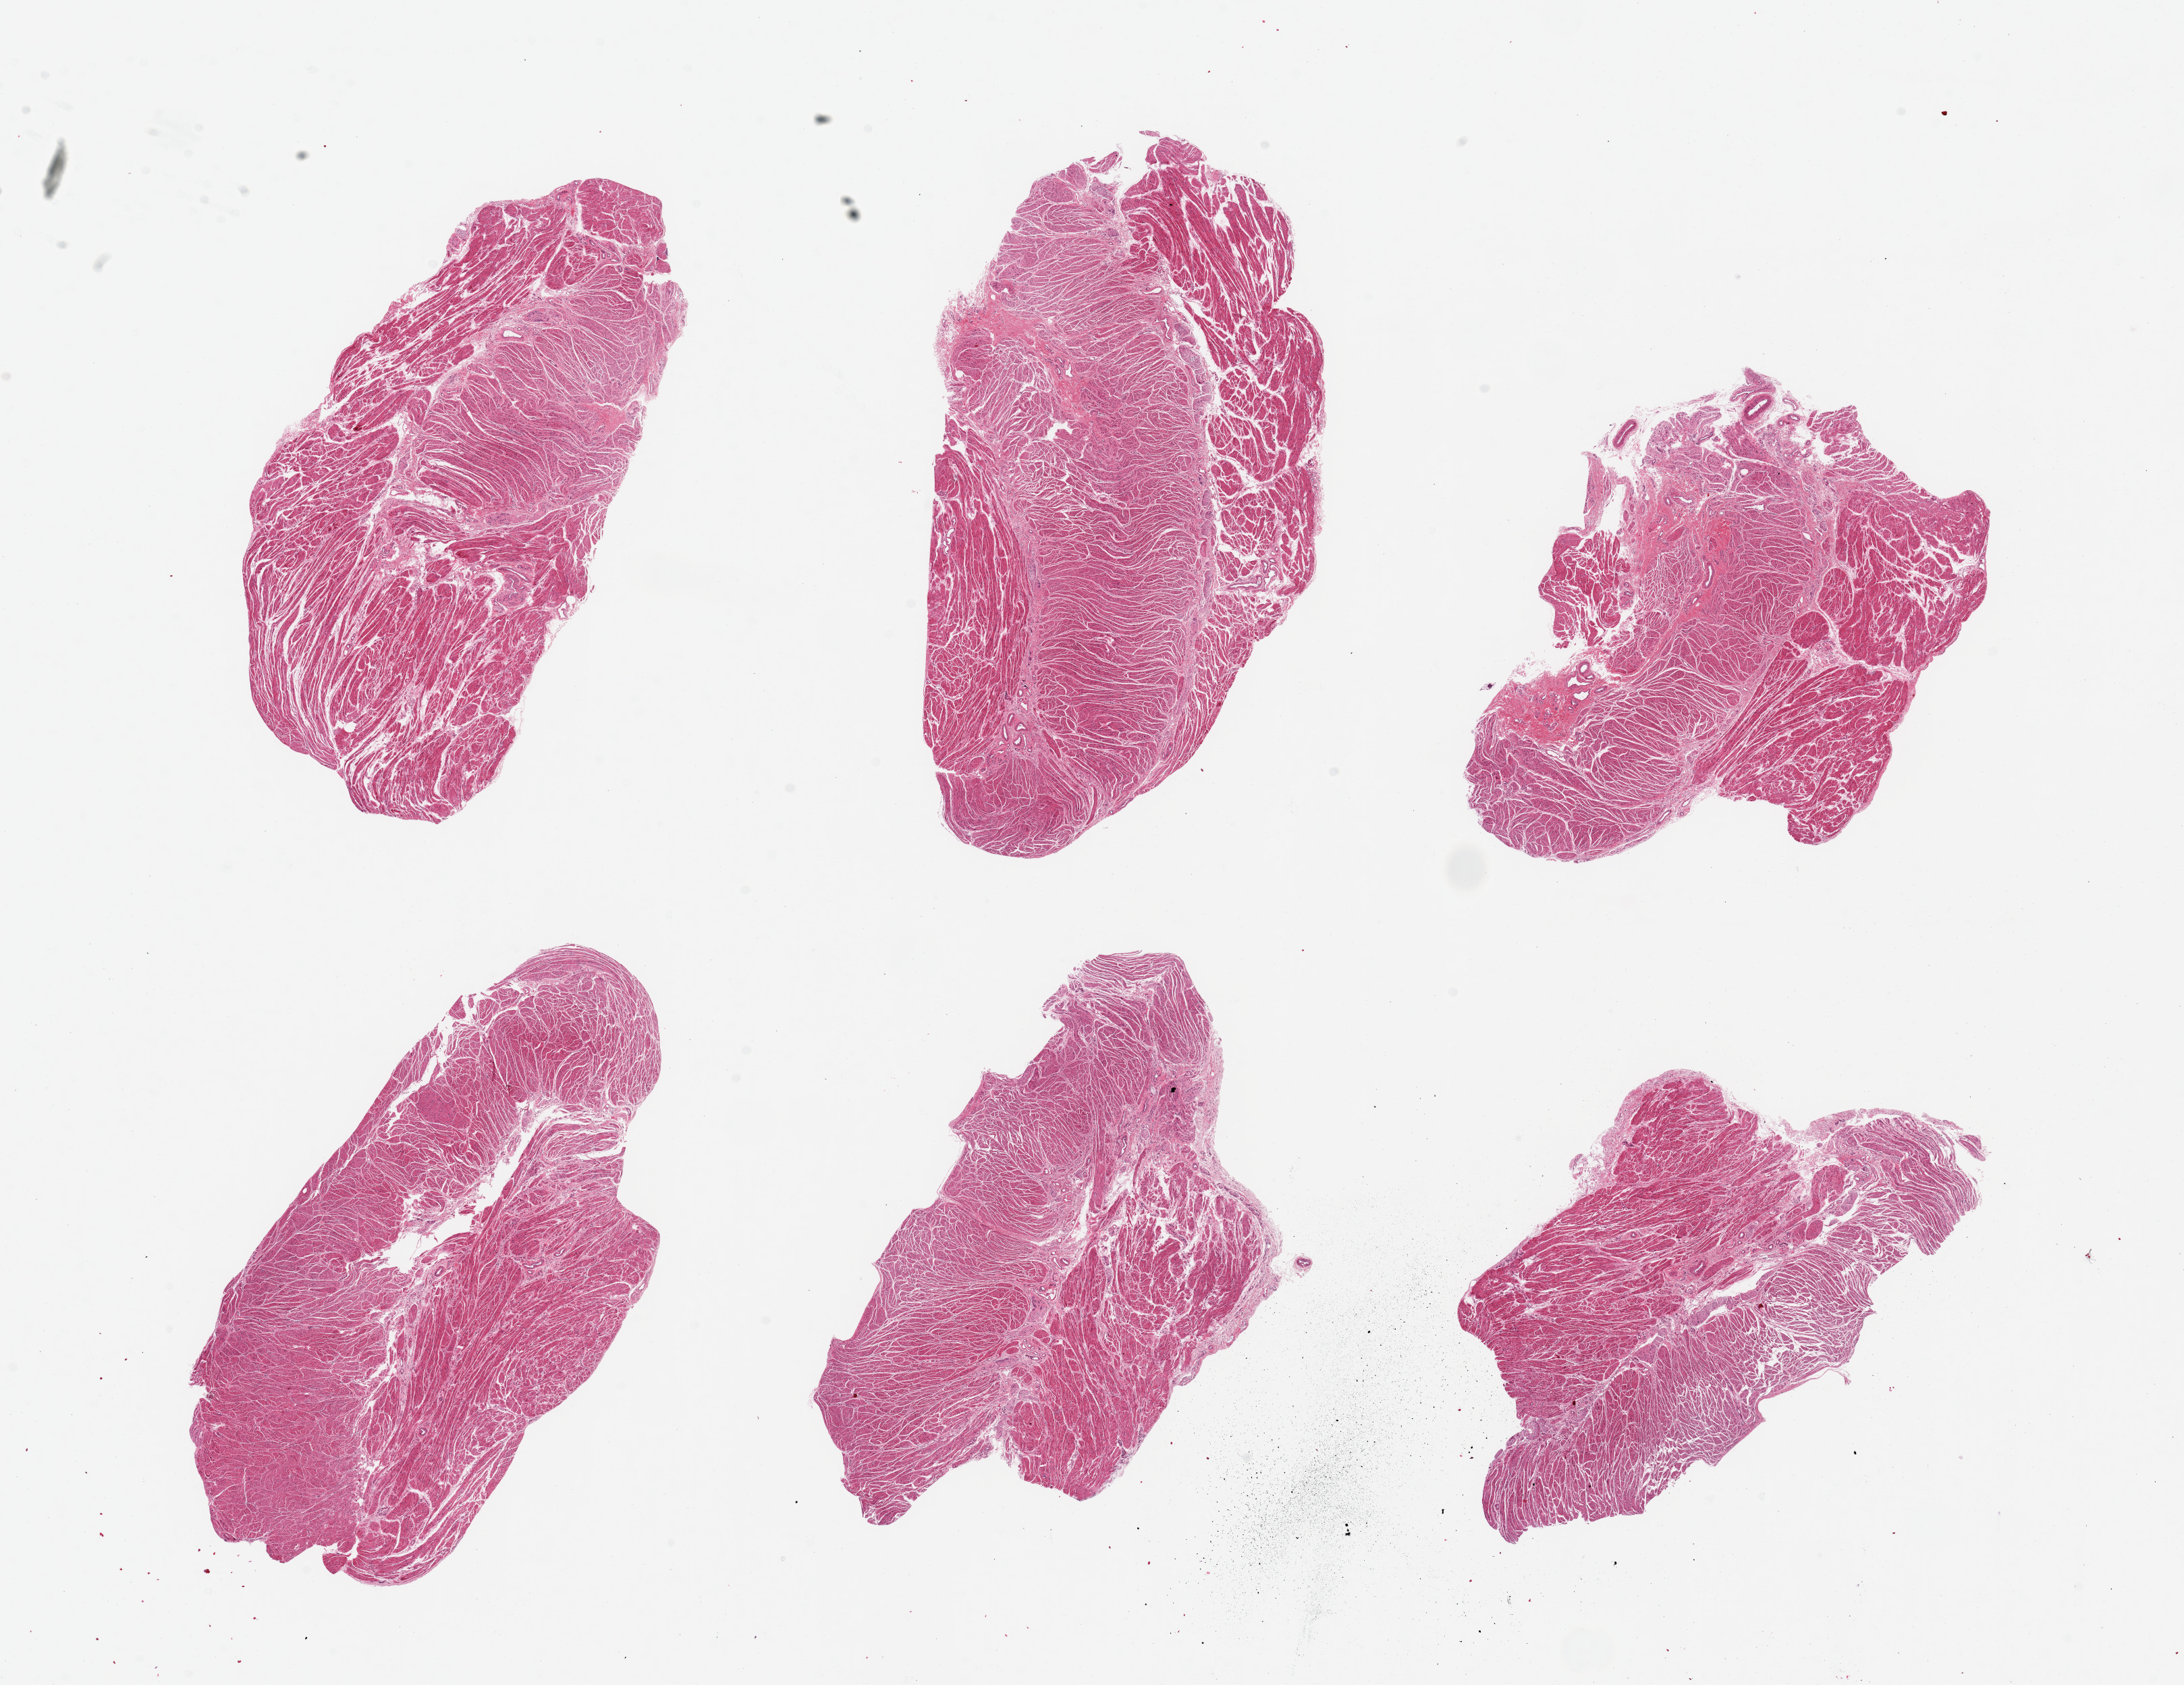
Hematoxylin and eosin (H&E) whole-slide image, a low-resolution overview of the entire scanned area, about 25.6 x 19.7 mm, PAXgene-fixed paraffin-embedded (PFPE) section, target tissue: gastroesophageal junction, tissue donor sample. Donor sex: female.
• pathologist's review note for this sample: 6 pieces, up to 7x3mm all muscularis, good specimens